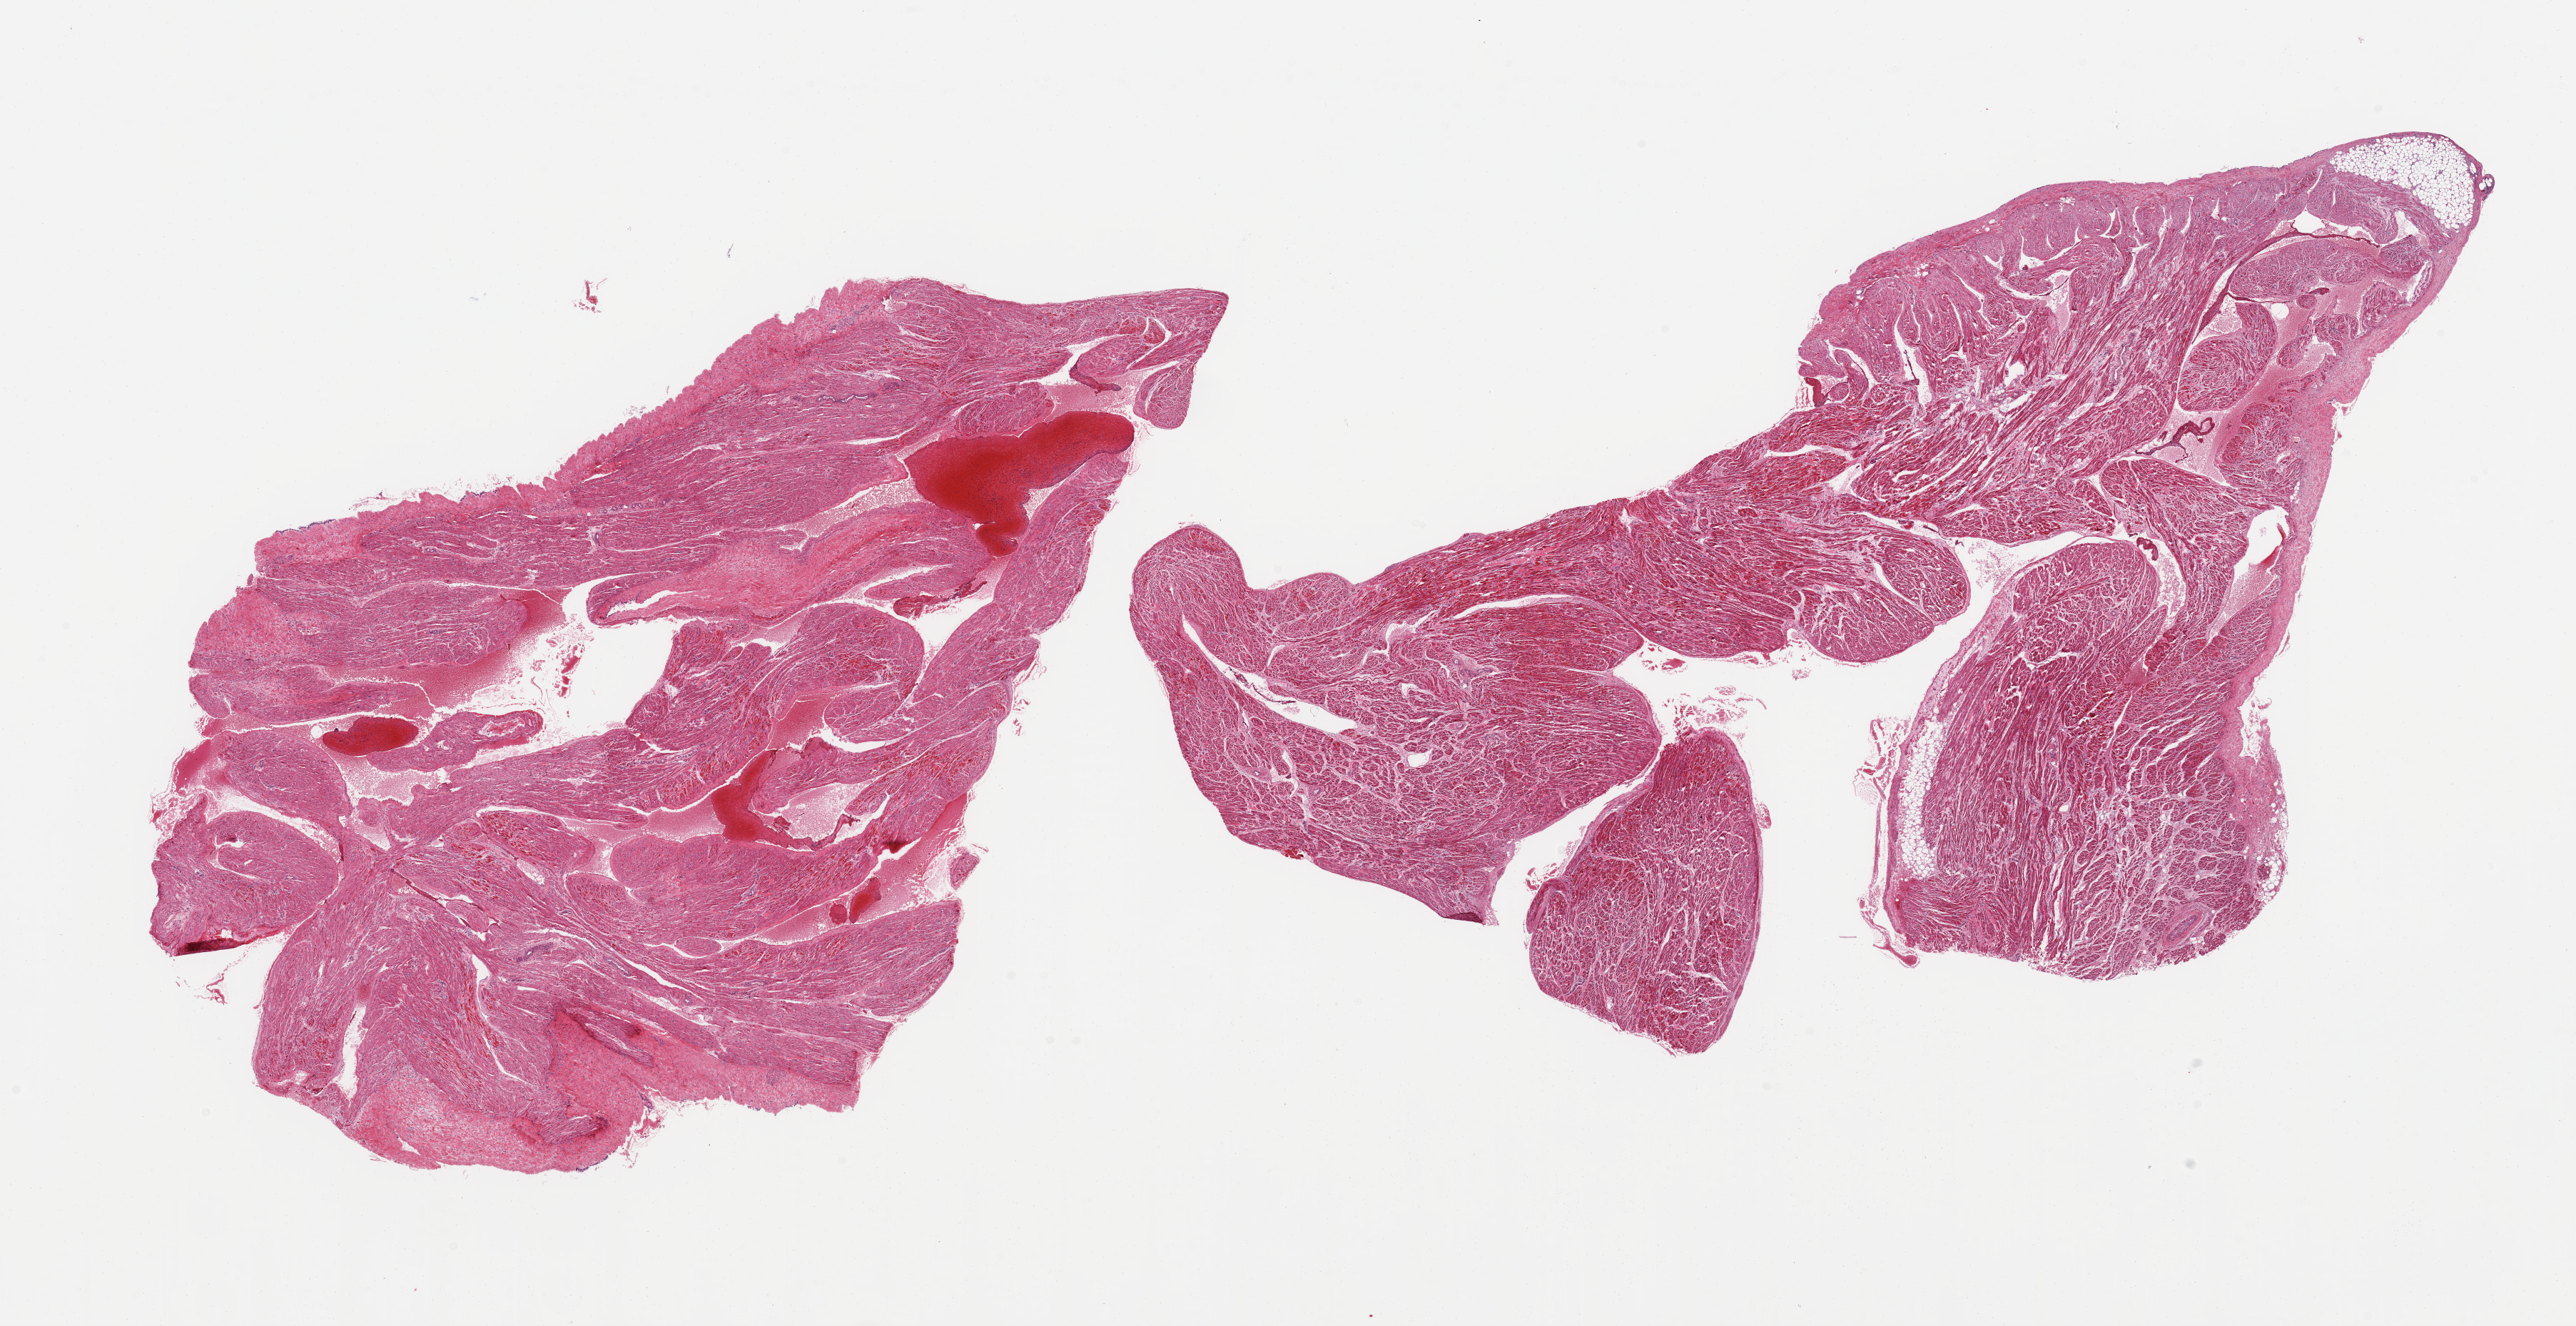
Whole-slide image, hematoxylin and eosin (H&E) stain, brightfield, whole scanned area (about 28.5 x 14.7 mm, acquisition: 20x scan) shown as a low-resolution overview; PAXgene-fixed, paraffin-embedded tissue; target tissue: auricular appendage; donor tissue sample.
Pathologist's review note for this sample: 2 pieces, no abnormalities.